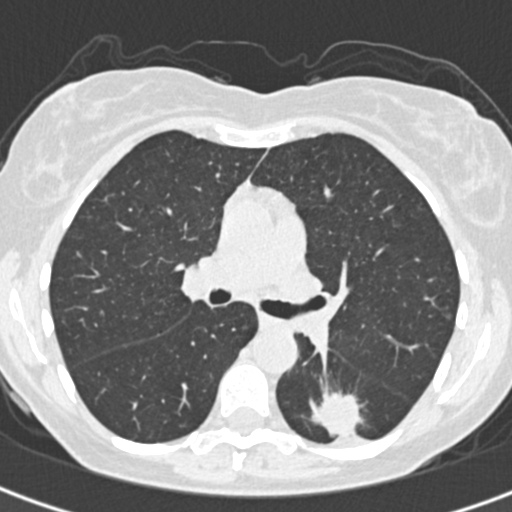
Low-dose screening chest CT, one axial slice; position 203 of 328 along the scan axis; reconstruction kernel B30f; 120 kVp; lung window (W 1500 / L -600 HU); 1 mm slice thickness; 512 × 512 image matrix, field of view 284 × 284 mm.
Structures marked on this image (outlined manually by an expert reader):
- lesion 1 (tumor, lower lobe of left lung): box from (x=311, y=392) to (x=362, y=437) px